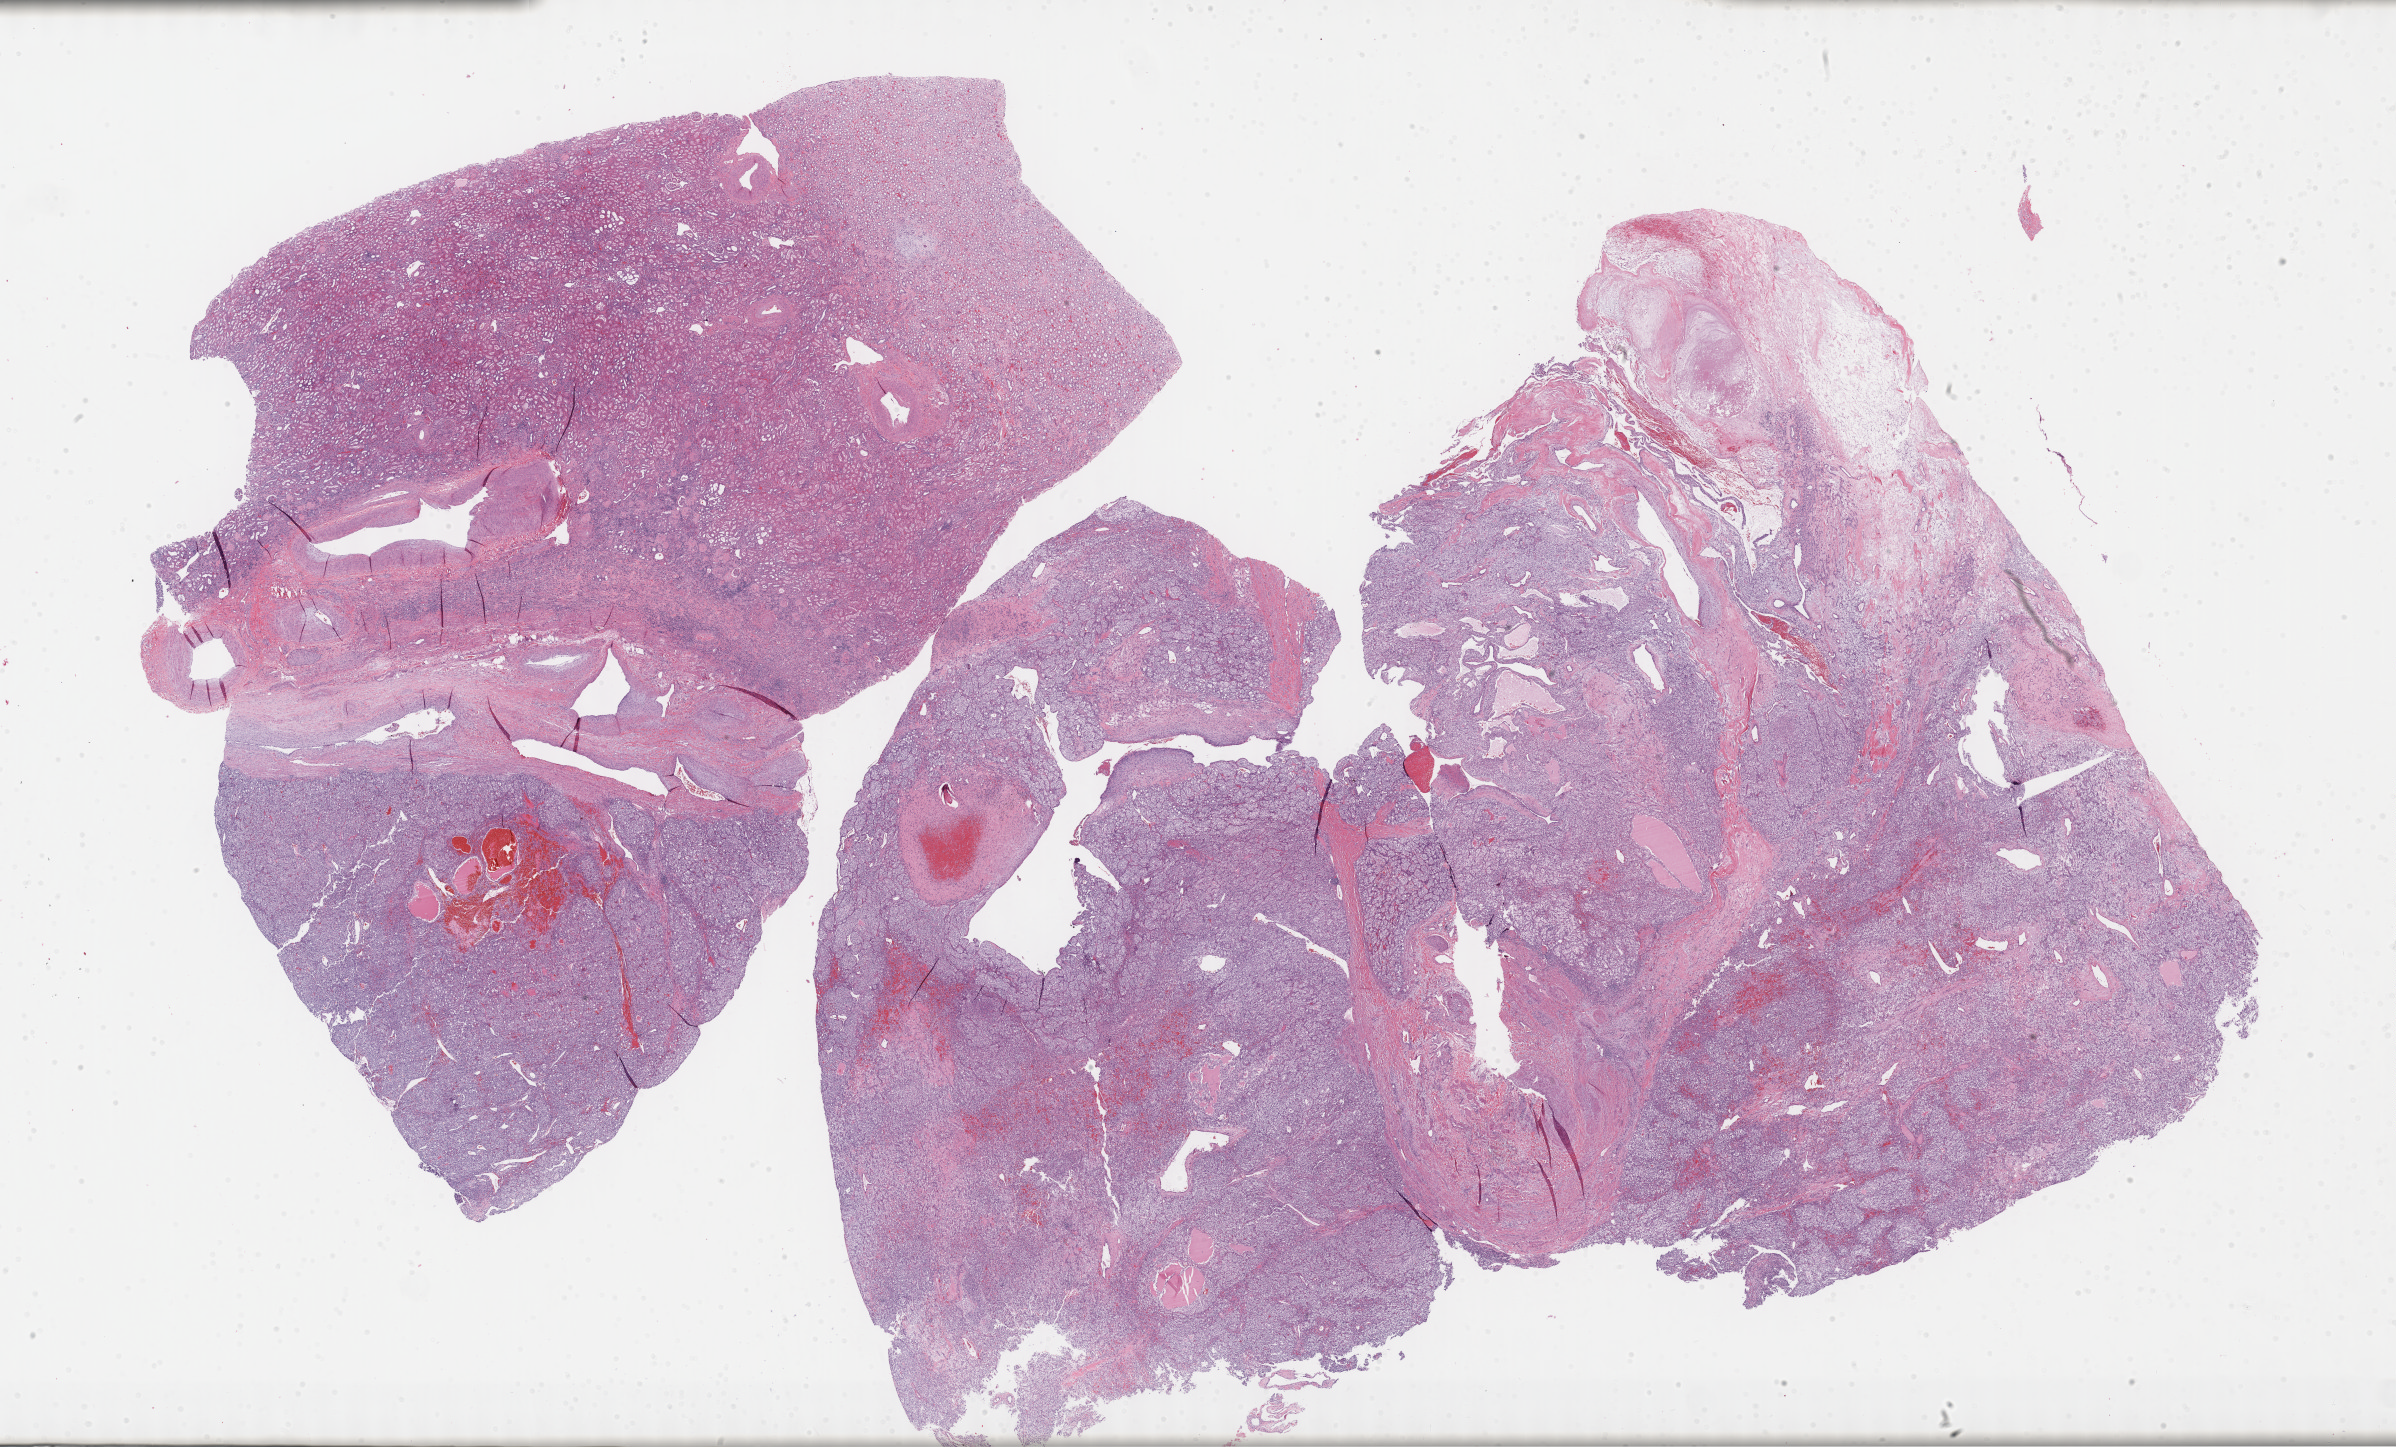
Whole-slide histology image, Hematoxylin and eosin (H&E) stained, a low-resolution overview of the entire scanned area, about 38.8 x 23.4 mm; formalin-fixed paraffin-embedded (FFPE) diagnostic section; kidney, primary tumour sample. Male patient; age at initial diagnosis 68 years.
Diagnosis: Clear cell adenocarcinoma, NOS.